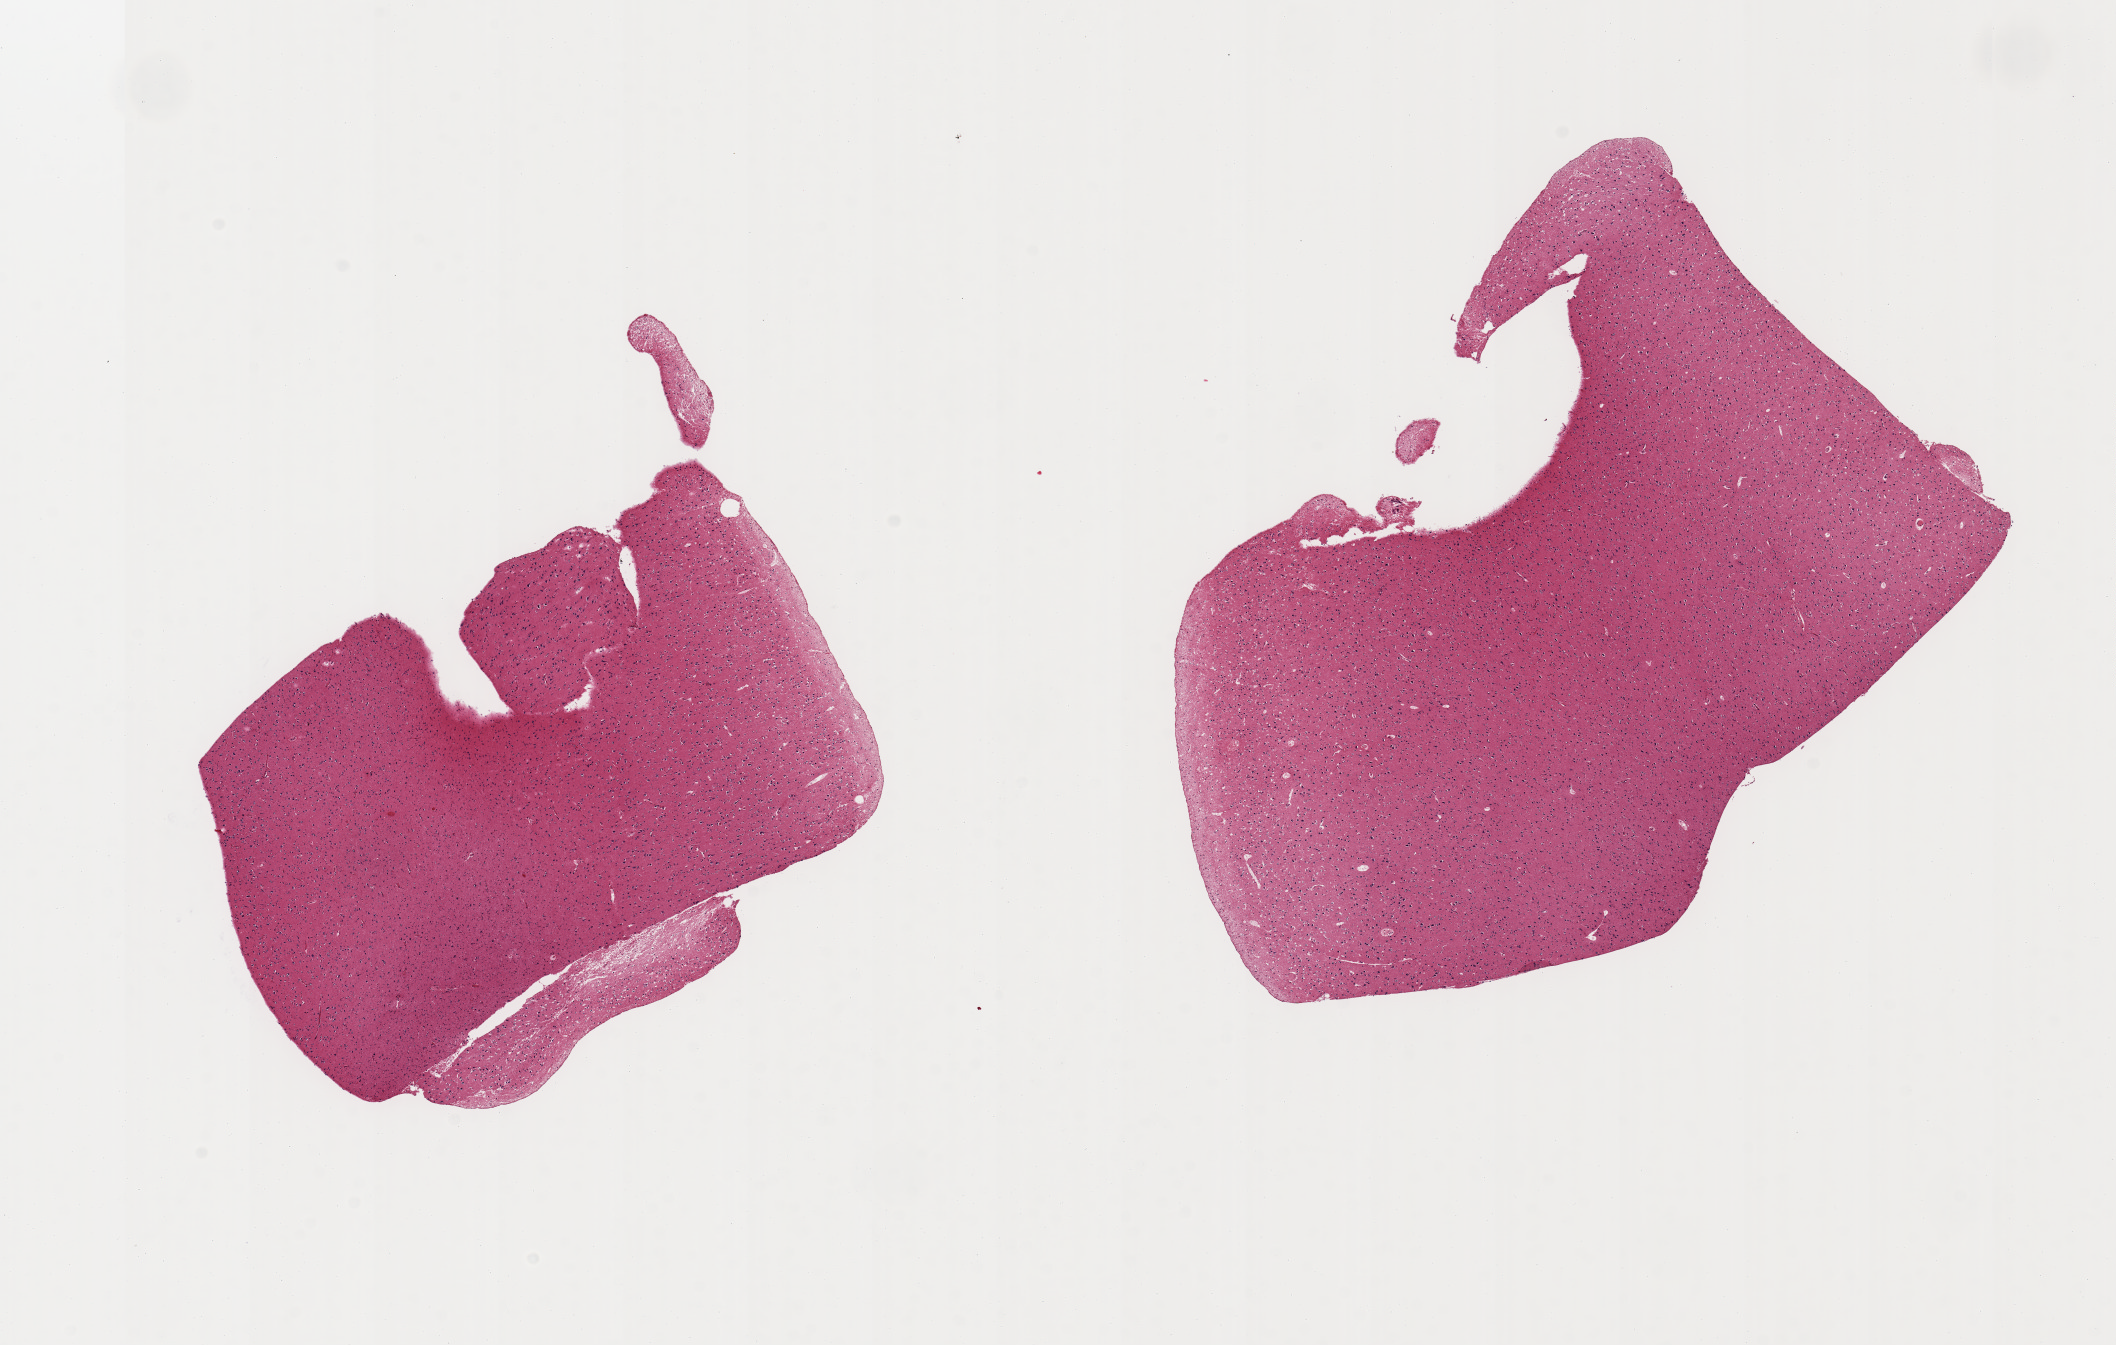
Digitized hematoxylin and eosin (H&E)-stained section, brightfield — low-resolution overview of the scanned area, about 16.7 x 10.6 mm. PAXgene-fixed paraffin-embedded (PFPE) section. Section of cerebral cortex (target tissue). Donor tissue sample. Male donor.
Review note (as recorded): 2 pieces; moderate autolysis.